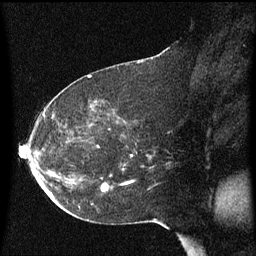
Breast MRI (dynamic contrast-enhanced), one sagittal slice. Slice 32 of 60 in the series (ordered by position). Dynamic contrast-enhanced series, image 2 of 3 at this slice position (ordered by acquisition). 1.5 T. TE 4.2 ms, TR 8.4 ms. 256 × 256 image matrix, field of view 200 × 200 mm. Female patient, age 54 years. Case-level facts recorded for this patient, not image findings: setting: breast cancer imaged before/during neoadjuvant chemotherapy; receptor status: HR-positive, HER2-negative.
Annotated regions visible in this slice (semi-automatic segmentation, software-assisted and operator-edited):
- analysis volume of interest (the breast-tissue region the enhancement analysis was run in; not a lesion): bounding box <97,120,134,191> (left, top, right, bottom; pixels)
- tumour enhancement mask (voxels above the 70 % enhancement threshold inside the analysis volume of interest): <103,186,109,191>